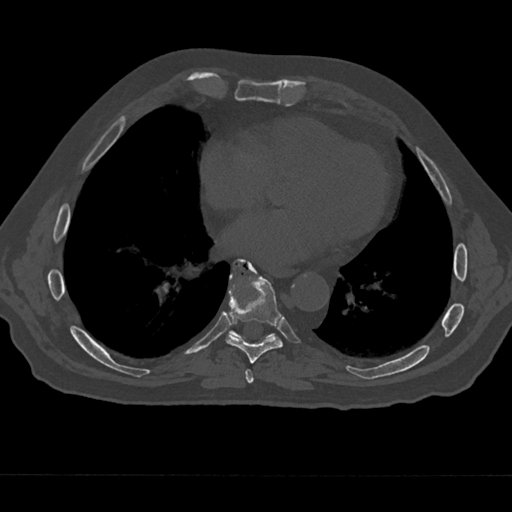
CT including the spine, one axial slice. Slice 304 of 797 in the series (ordered by position). Reconstruction kernel Br40s/3. Bone window (W 1800 / L 400 HU). 0.5 mm slice thickness. 512 × 512 image matrix, field of view 377 × 377 mm. Patient: male, 75 years. From the clinical record (not read from this slice): primary cancer: renal.
Annotated regions visible in this slice (semi-automatic segmentation, software-assisted and operator-edited):
- T7 vertebra: bounding box [x1, y1, x2, y2] px = [241, 367, 255, 384]
- T8 vertebra: [226, 263, 283, 363]
- T9 vertebra: [229, 259, 275, 338]